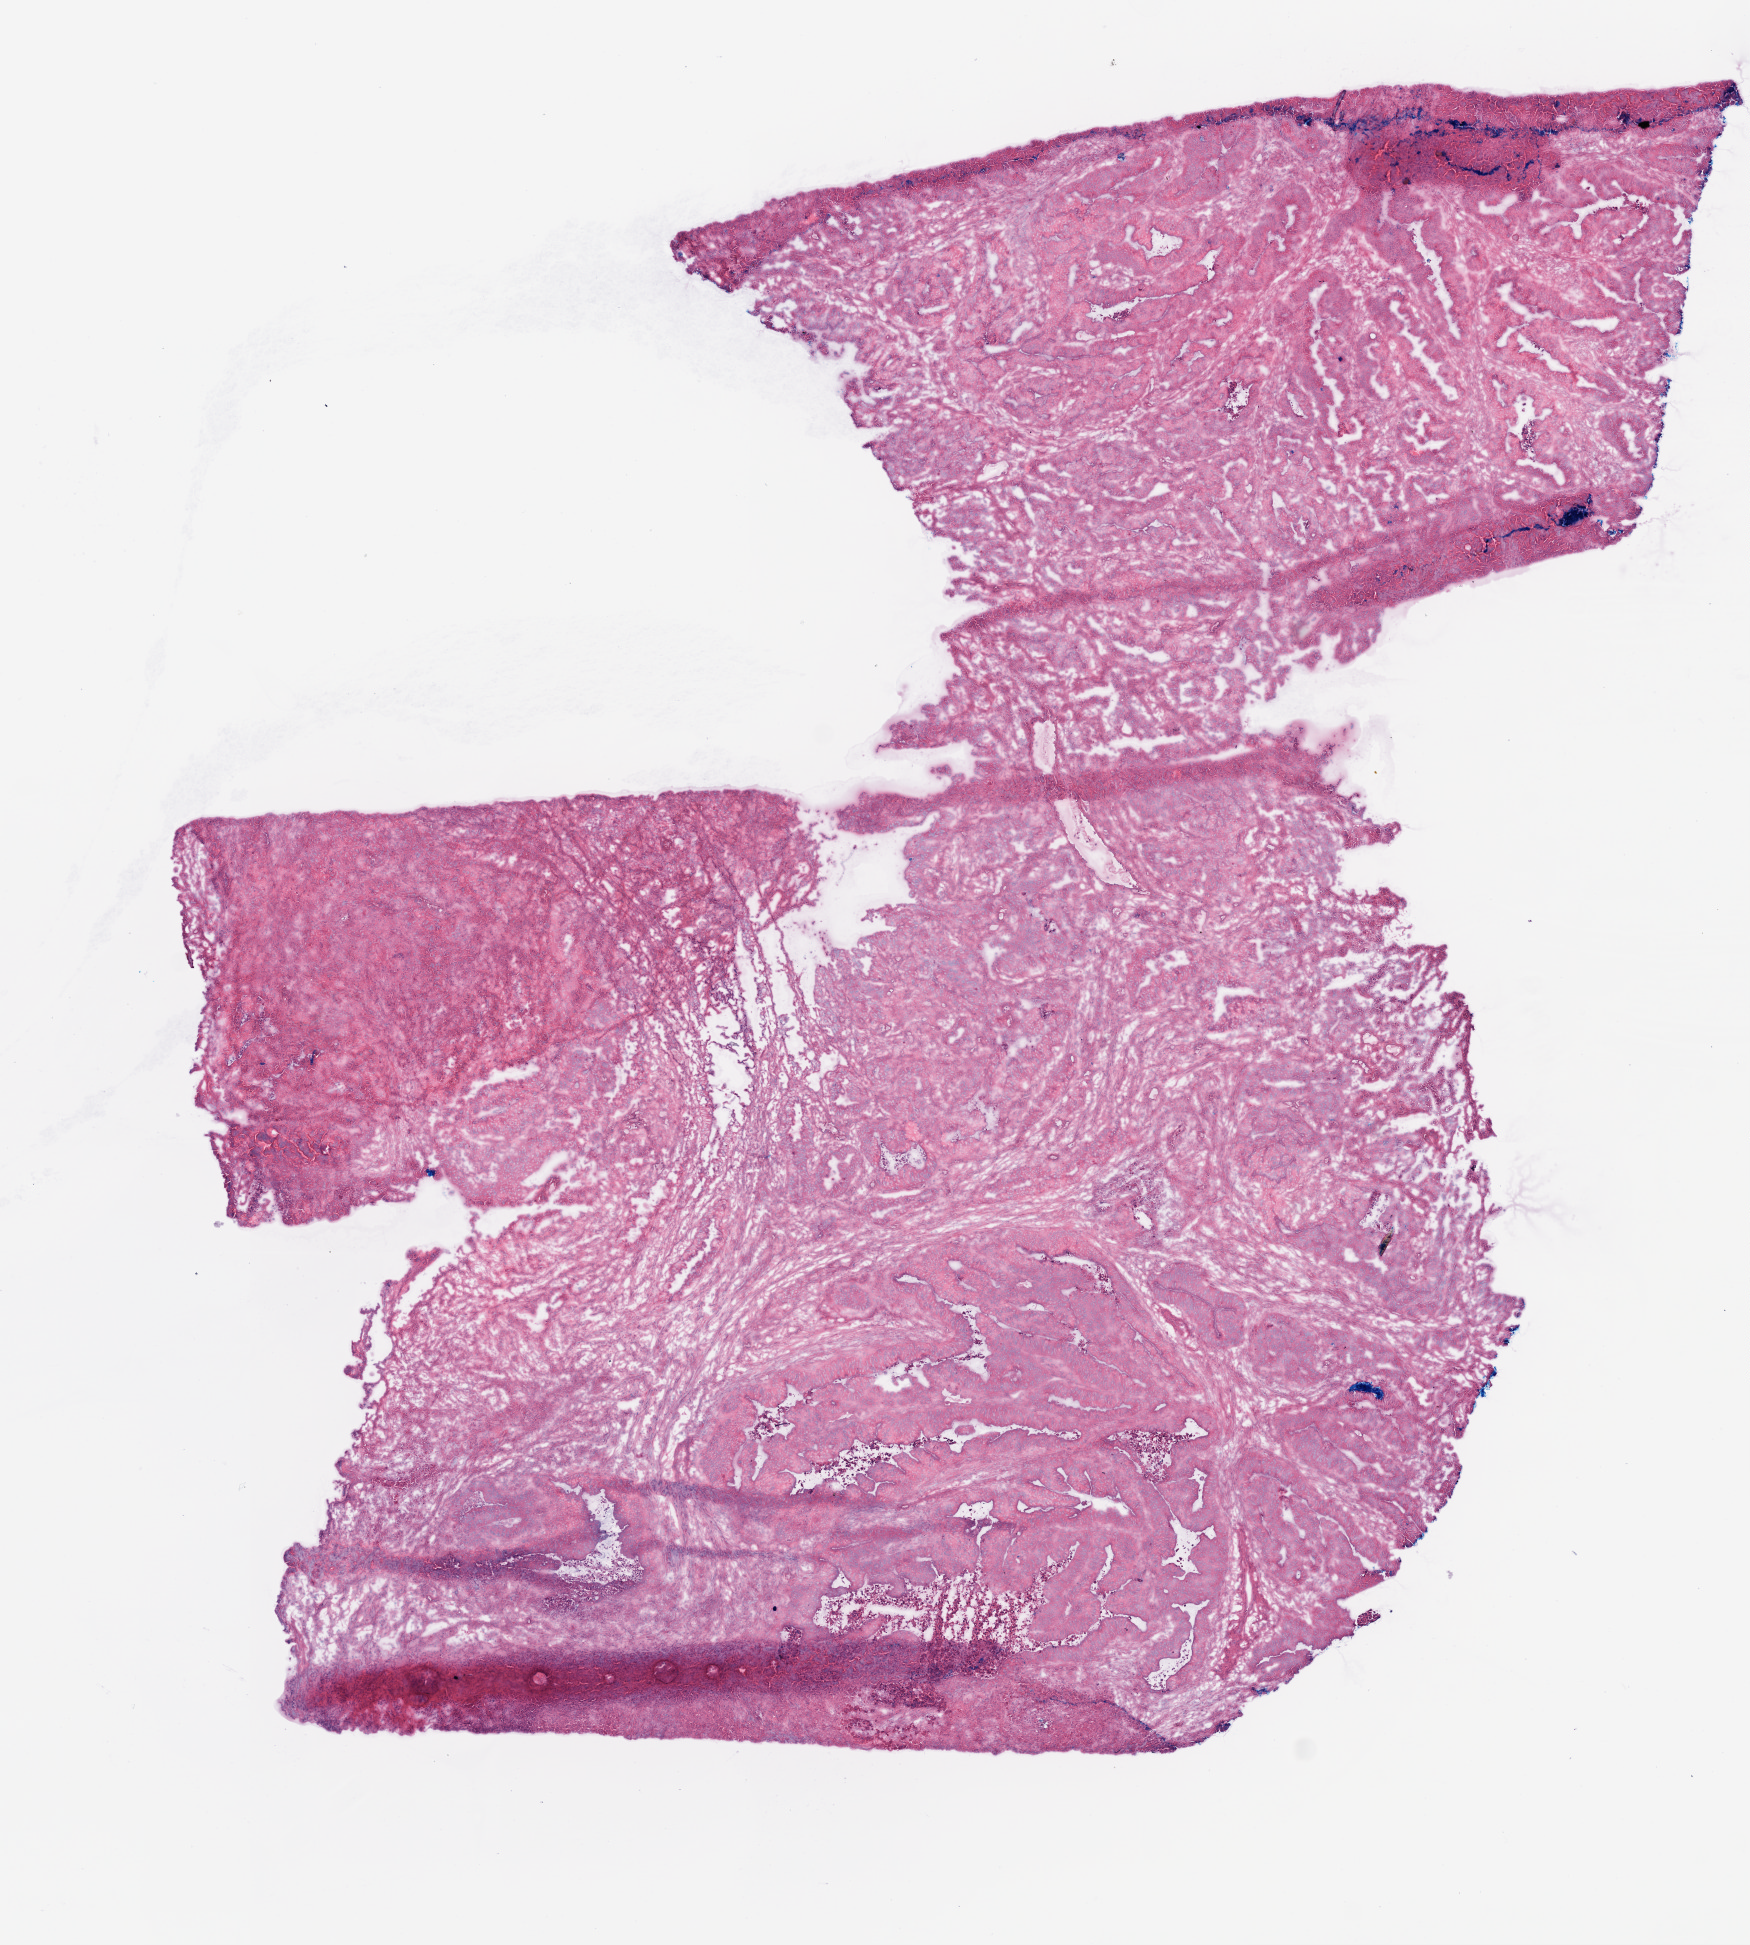
Whole-slide histology image, H&E-stained, low-resolution overview of the scanned area, about 7.0 x 7.8 mm; frozen section from the top of the tissue portion; primary tumour sample from the colon. Female patient; age at initial diagnosis 78 years. Slide review estimates, as recorded: tumour cells 77%, tumour nuclei 85%, normal cells 0%, stromal cells 15%, necrosis 8%.
Lymph nodes positive (case pathology): 0 of 23 examined. AJCC pathologic stage: I (5th edition). Histologic diagnosis: Adenocarcinoma, NOS. TNM: T2 N0 M0.